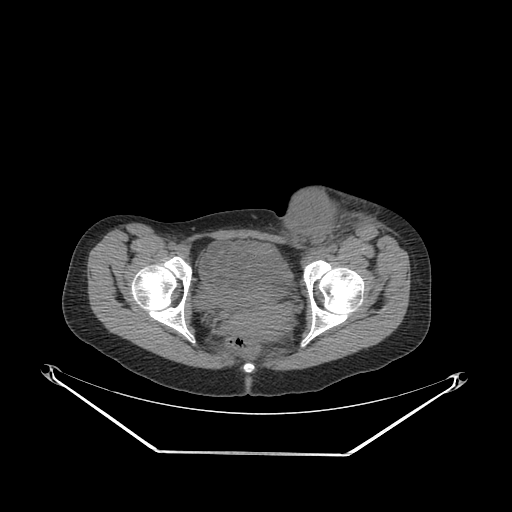
CT of an extremity soft-tissue mass (from a PET/CT study), one axial slice; slice 72 of 267 in the series (ordered by position); reconstruction kernel SOFT; 140 kVp; soft-tissue window (W 400 / L 40 HU); 3.75 mm slice thickness; 512 × 512 image matrix. Female patient. Case-level facts recorded for this patient, not image findings: histological type: leiomyosarcoma; grade: high; site of the primary tumour: groin.
Annotated regions visible in this slice (expert contour drawn on MRI and transferred to this co-registered scan by the dataset authors):
- gross tumour volume including surrounding oedema: bounding box <276,192,385,264> (left, top, right, bottom; pixels)
- gross tumour volume (mass): <276,194,343,252>